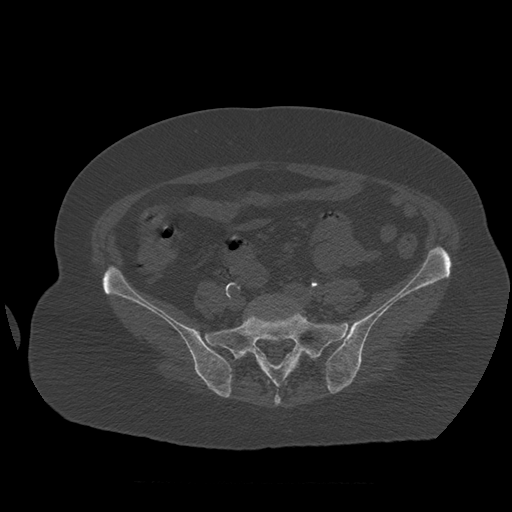
CT including the spine, one axial slice. Position 167 of 399 along the scan axis. 120 kVp. Bone window (W 1800 / L 400 HU). 1.25 mm slice thickness. 512 × 512 image matrix, field of view 404 × 404 mm. Patient age 81 years. From the clinical record (not read from this slice): primary cancer: renal.
Annotated regions visible in this slice (semi-automatic segmentation, software-assisted and operator-edited):
- L5 vertebra: bounding box [x1, y1, x2, y2] px = [268, 295, 274, 298]